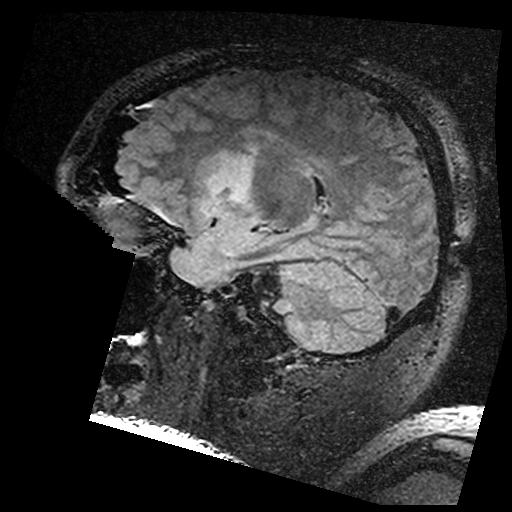
Brain MRI from a brain-tumour surgery series, one sagittal slice; position 112 of 176 along the scan axis; T2 FLAIR; 1 mm slice thickness; 512 × 512 image matrix, field of view 250 × 250 mm. Case-level facts recorded for this patient, not image findings: histopathology: Astrocytoma; WHO grade: 3; IDH mutation: yes.
Structures marked on this image (outlined manually by an expert reader):
- residual tumour: bounding box (x1, y1, x2, y2) in pixels: (202, 149, 255, 200)